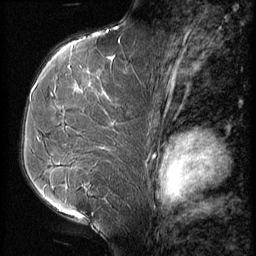
Breast MRI (dynamic contrast-enhanced), one sagittal slice; 3 images stored at this slice position (order not interpretable as contrast timing); 1.5 T; TE 4.2 ms, TR 9 ms; 2.5 mm slice thickness; 256 × 256 image matrix, field of view 180 × 180 mm. Patient: female, 51 years. From the clinical record (not read from this slice): setting: breast cancer imaged before/during neoadjuvant chemotherapy; receptor status: HR-positive, HER2-negative.
Structures marked on this image (semi-automatic segmentation, software-assisted and operator-edited):
- analysis volume of interest (the breast-tissue region the enhancement analysis was run in; not a lesion): bounding box [x1, y1, x2, y2] px = [23, 56, 147, 165]
- tumour enhancement mask (voxels above the 140 % enhancement threshold inside the analysis volume of interest): [35, 66, 112, 103]